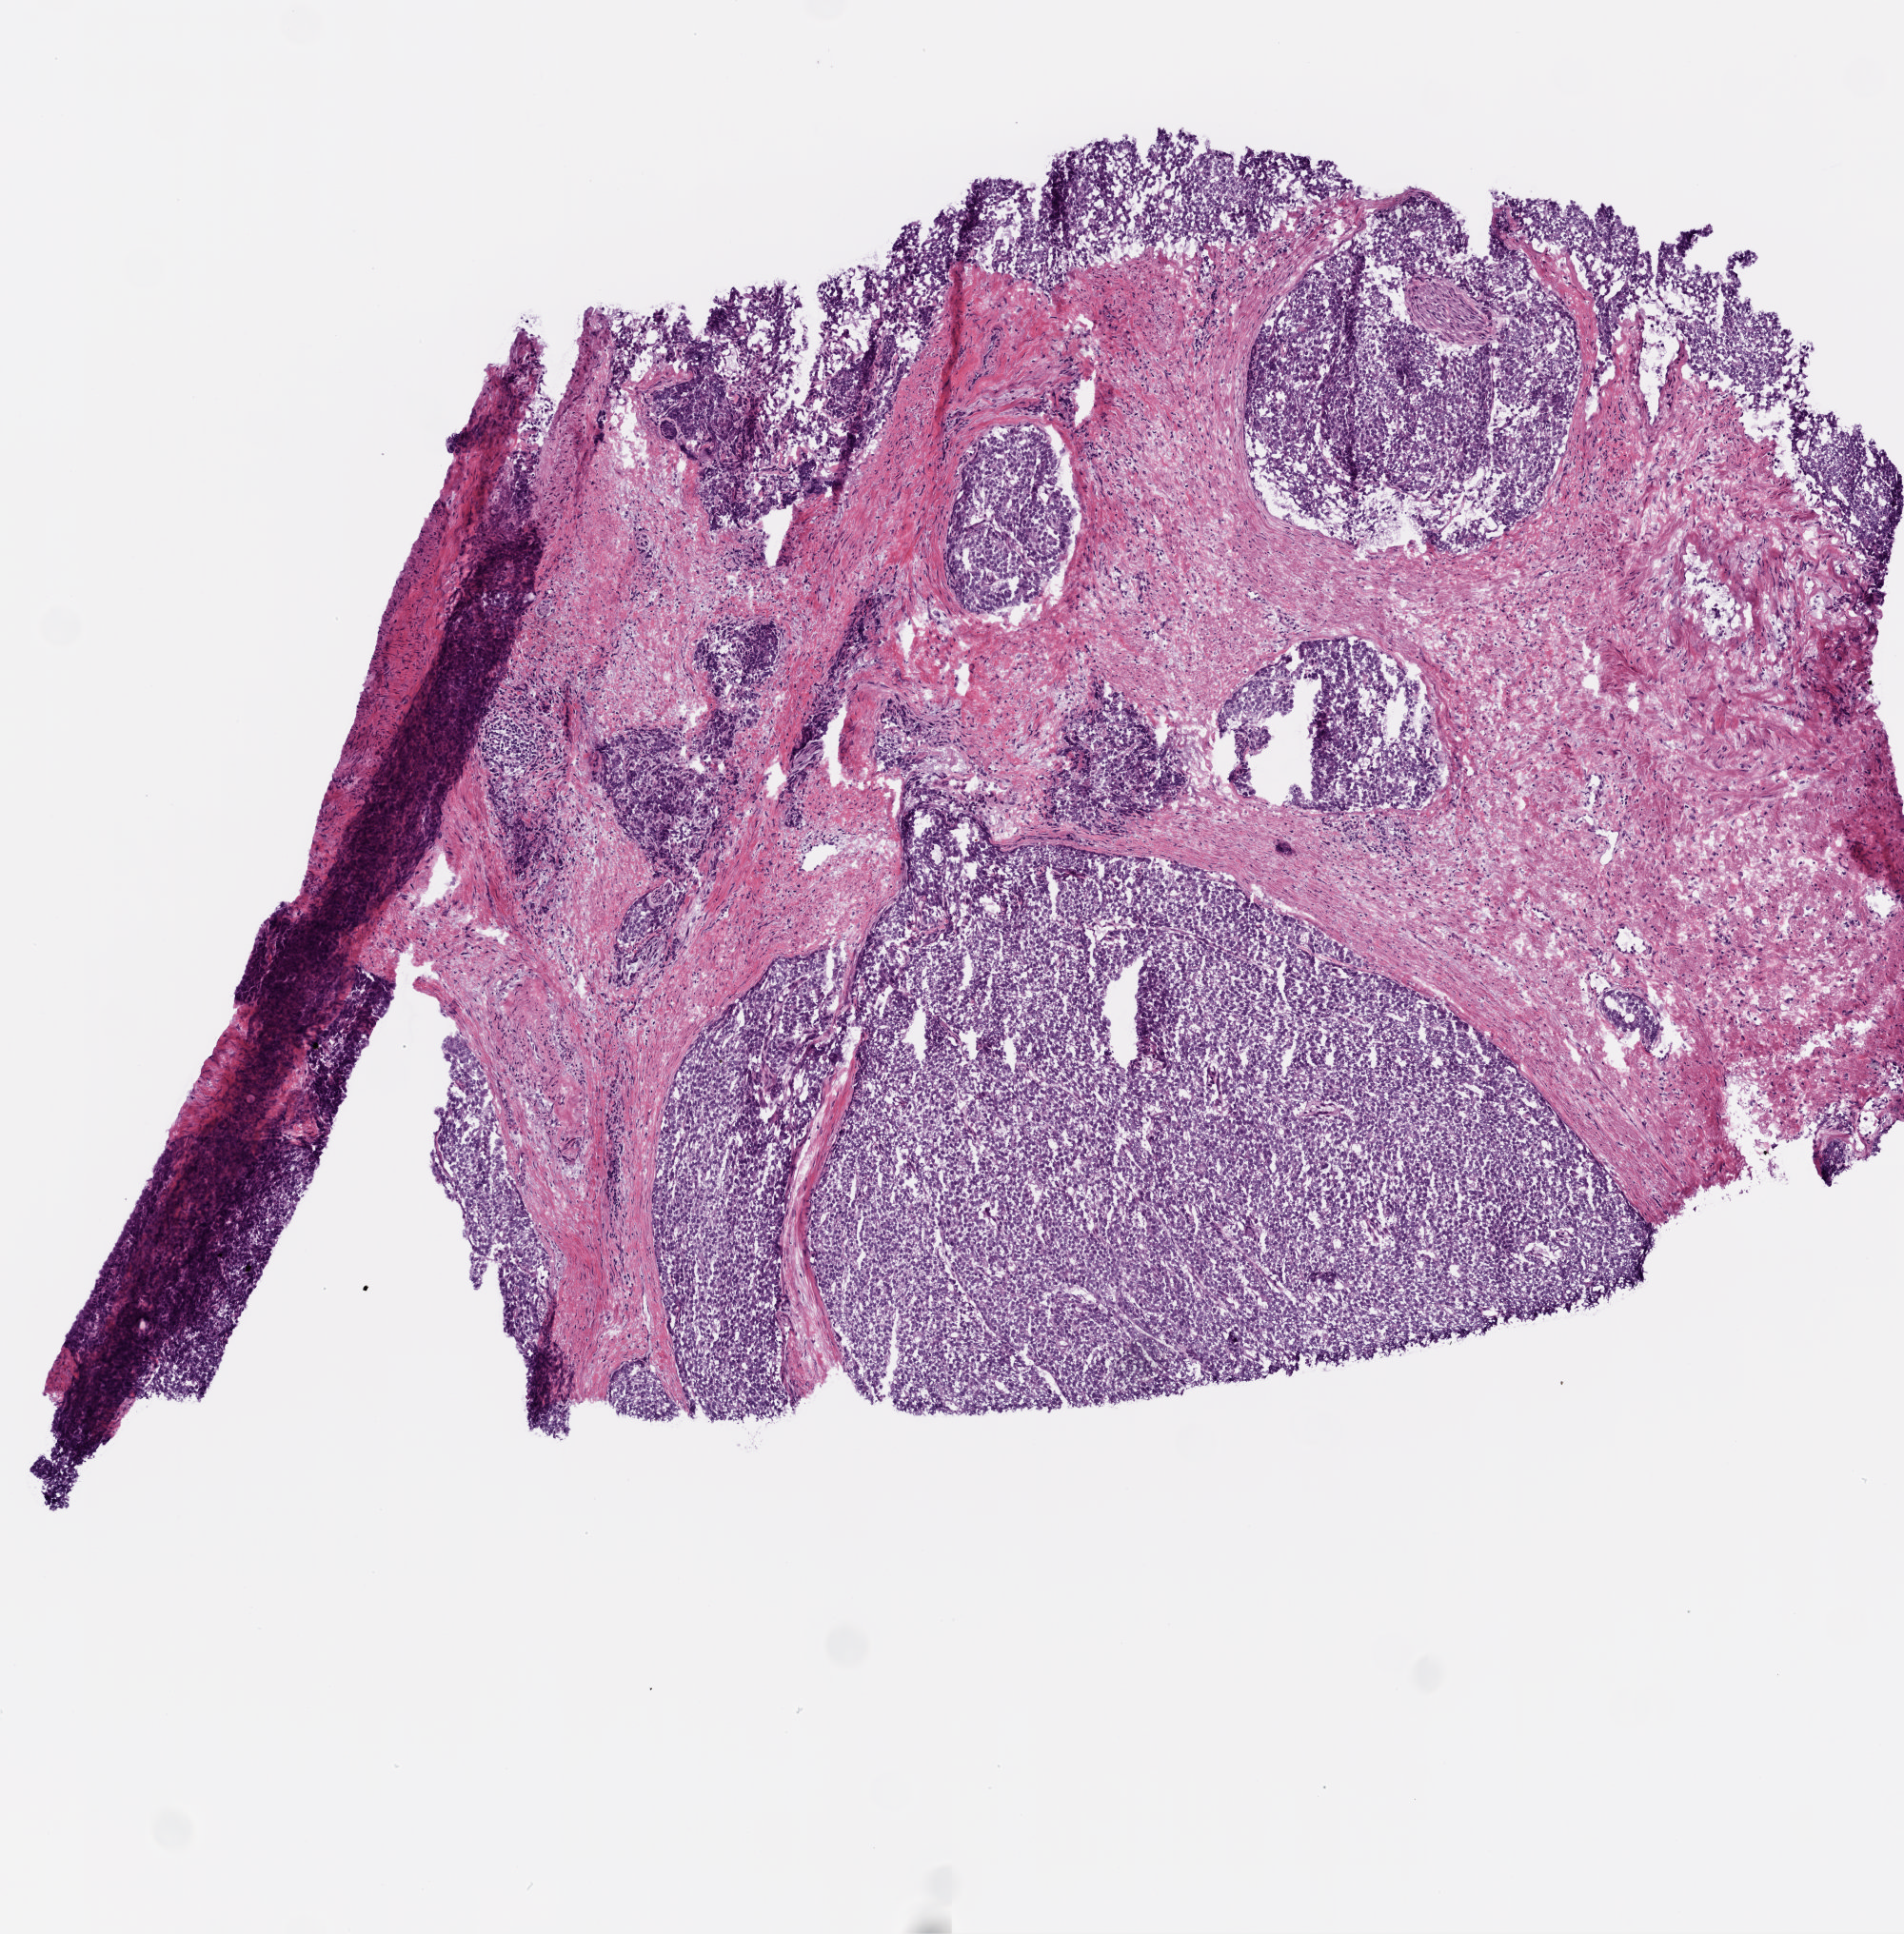
Digitized Hematoxylin and eosin (H&E) stained tissue section (whole slide) — low-resolution overview of the scanned area, about 4.0 x 4.1 mm. Frozen section. Primary tumour sample from the prostate. Male, age 66 years at initial diagnosis. Gleason score: 8 (4+4). Composition of this section per pathologist review: tumour cells 55%, tumour nuclei 70%, normal cells 0%, stromal cells 43%, necrosis 2%. Inflammatory infiltration, as recorded: lymphocyte infiltration 0%, monocyte infiltration 0%, neutrophil infiltration 0%.
Laterality: bilateral. Pathologic diagnosis: Acinar cell carcinoma. Lymph nodes positive (case pathology): 0 of 9 examined.